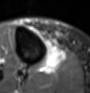
MRI of an extremity soft-tissue mass, one axial slice; slice 34 of 60 in the series (ordered by position); STIR; MR volume resampled by the dataset authors to the PET/CT grid (not the native acquisition matrix); 90 × 93 image matrix, field of view 88 × 91 mm. Female patient. Case-level facts recorded for this patient, not image findings: histological type: undifferentiated – high grade; grade: high; site of the primary tumour: right thigh.
Structures marked on this image (expert contour drawn on MRI and transferred to this co-registered scan by the dataset authors):
- gross tumour volume (mass): bounding box <42,46,66,73> (left, top, right, bottom; pixels)